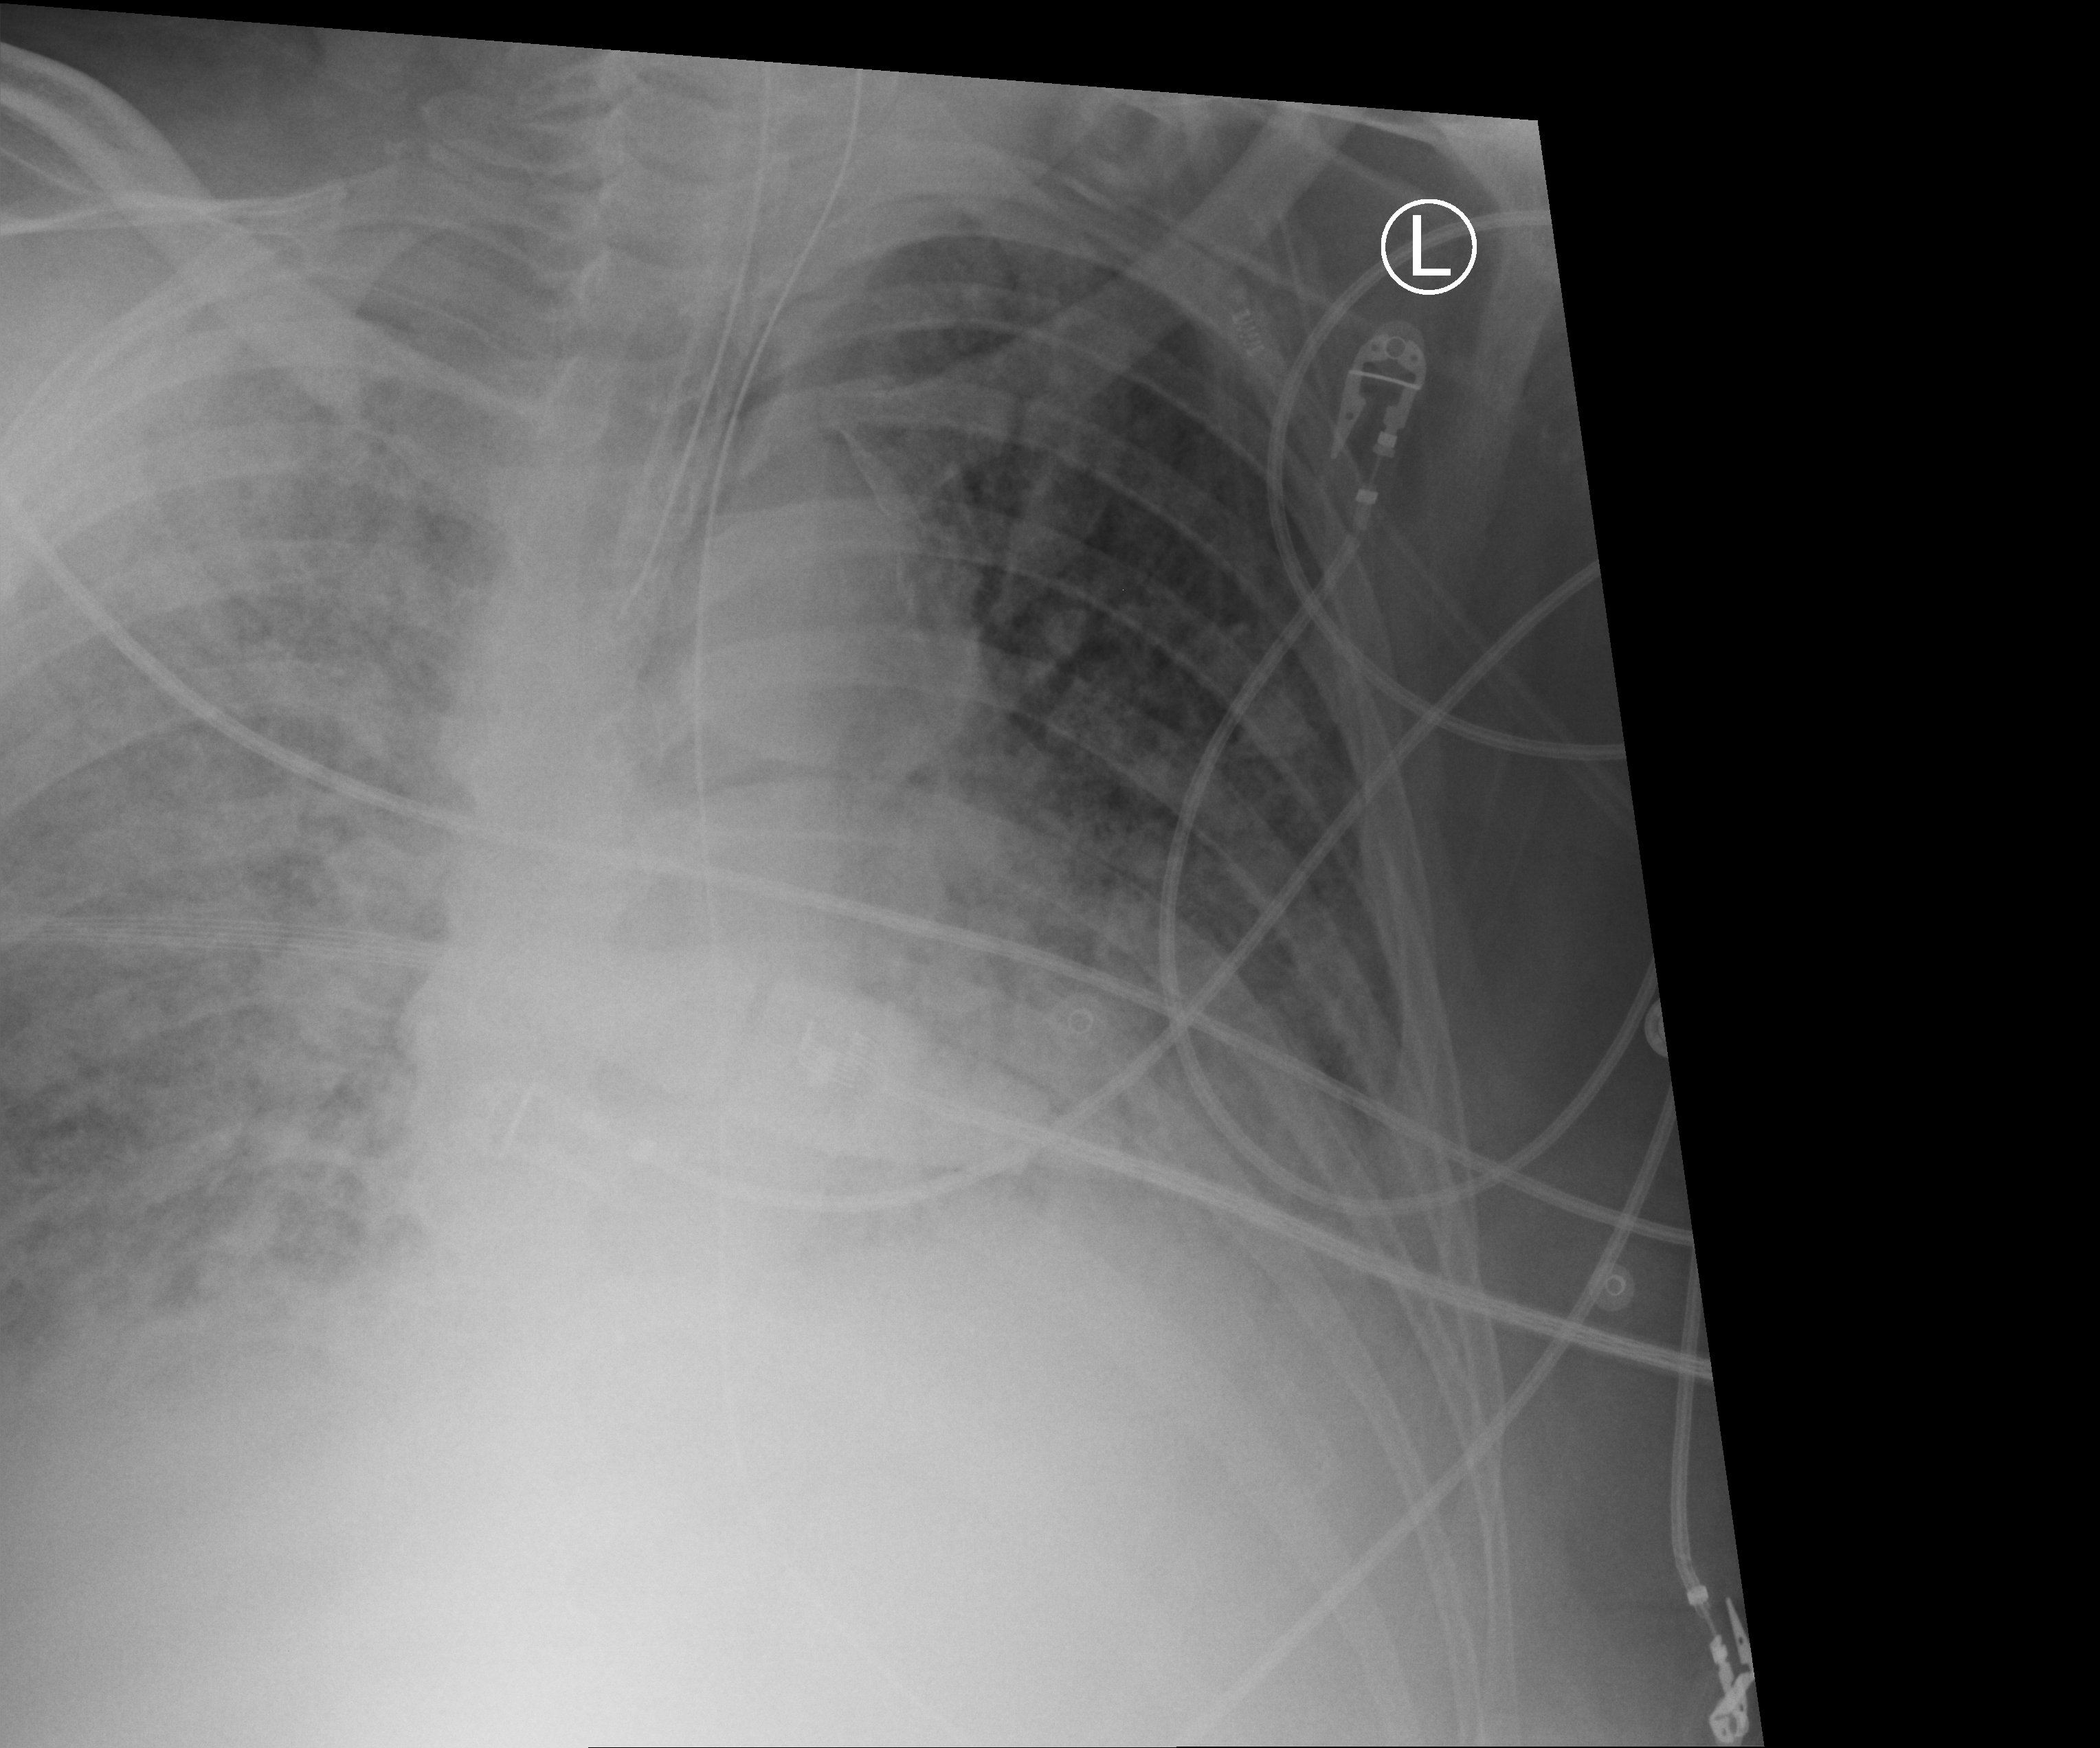
Portable chest radiograph; anteroposterior (AP) projection. Patient hospitalised with COVID-19; male, aged 60–74 years.
Hospital-stay facts (about this admission, not read from this image; timing relative to this image not recorded):
- hypertension (admission record): yes
- mechanically ventilated during this hospital stay: yes